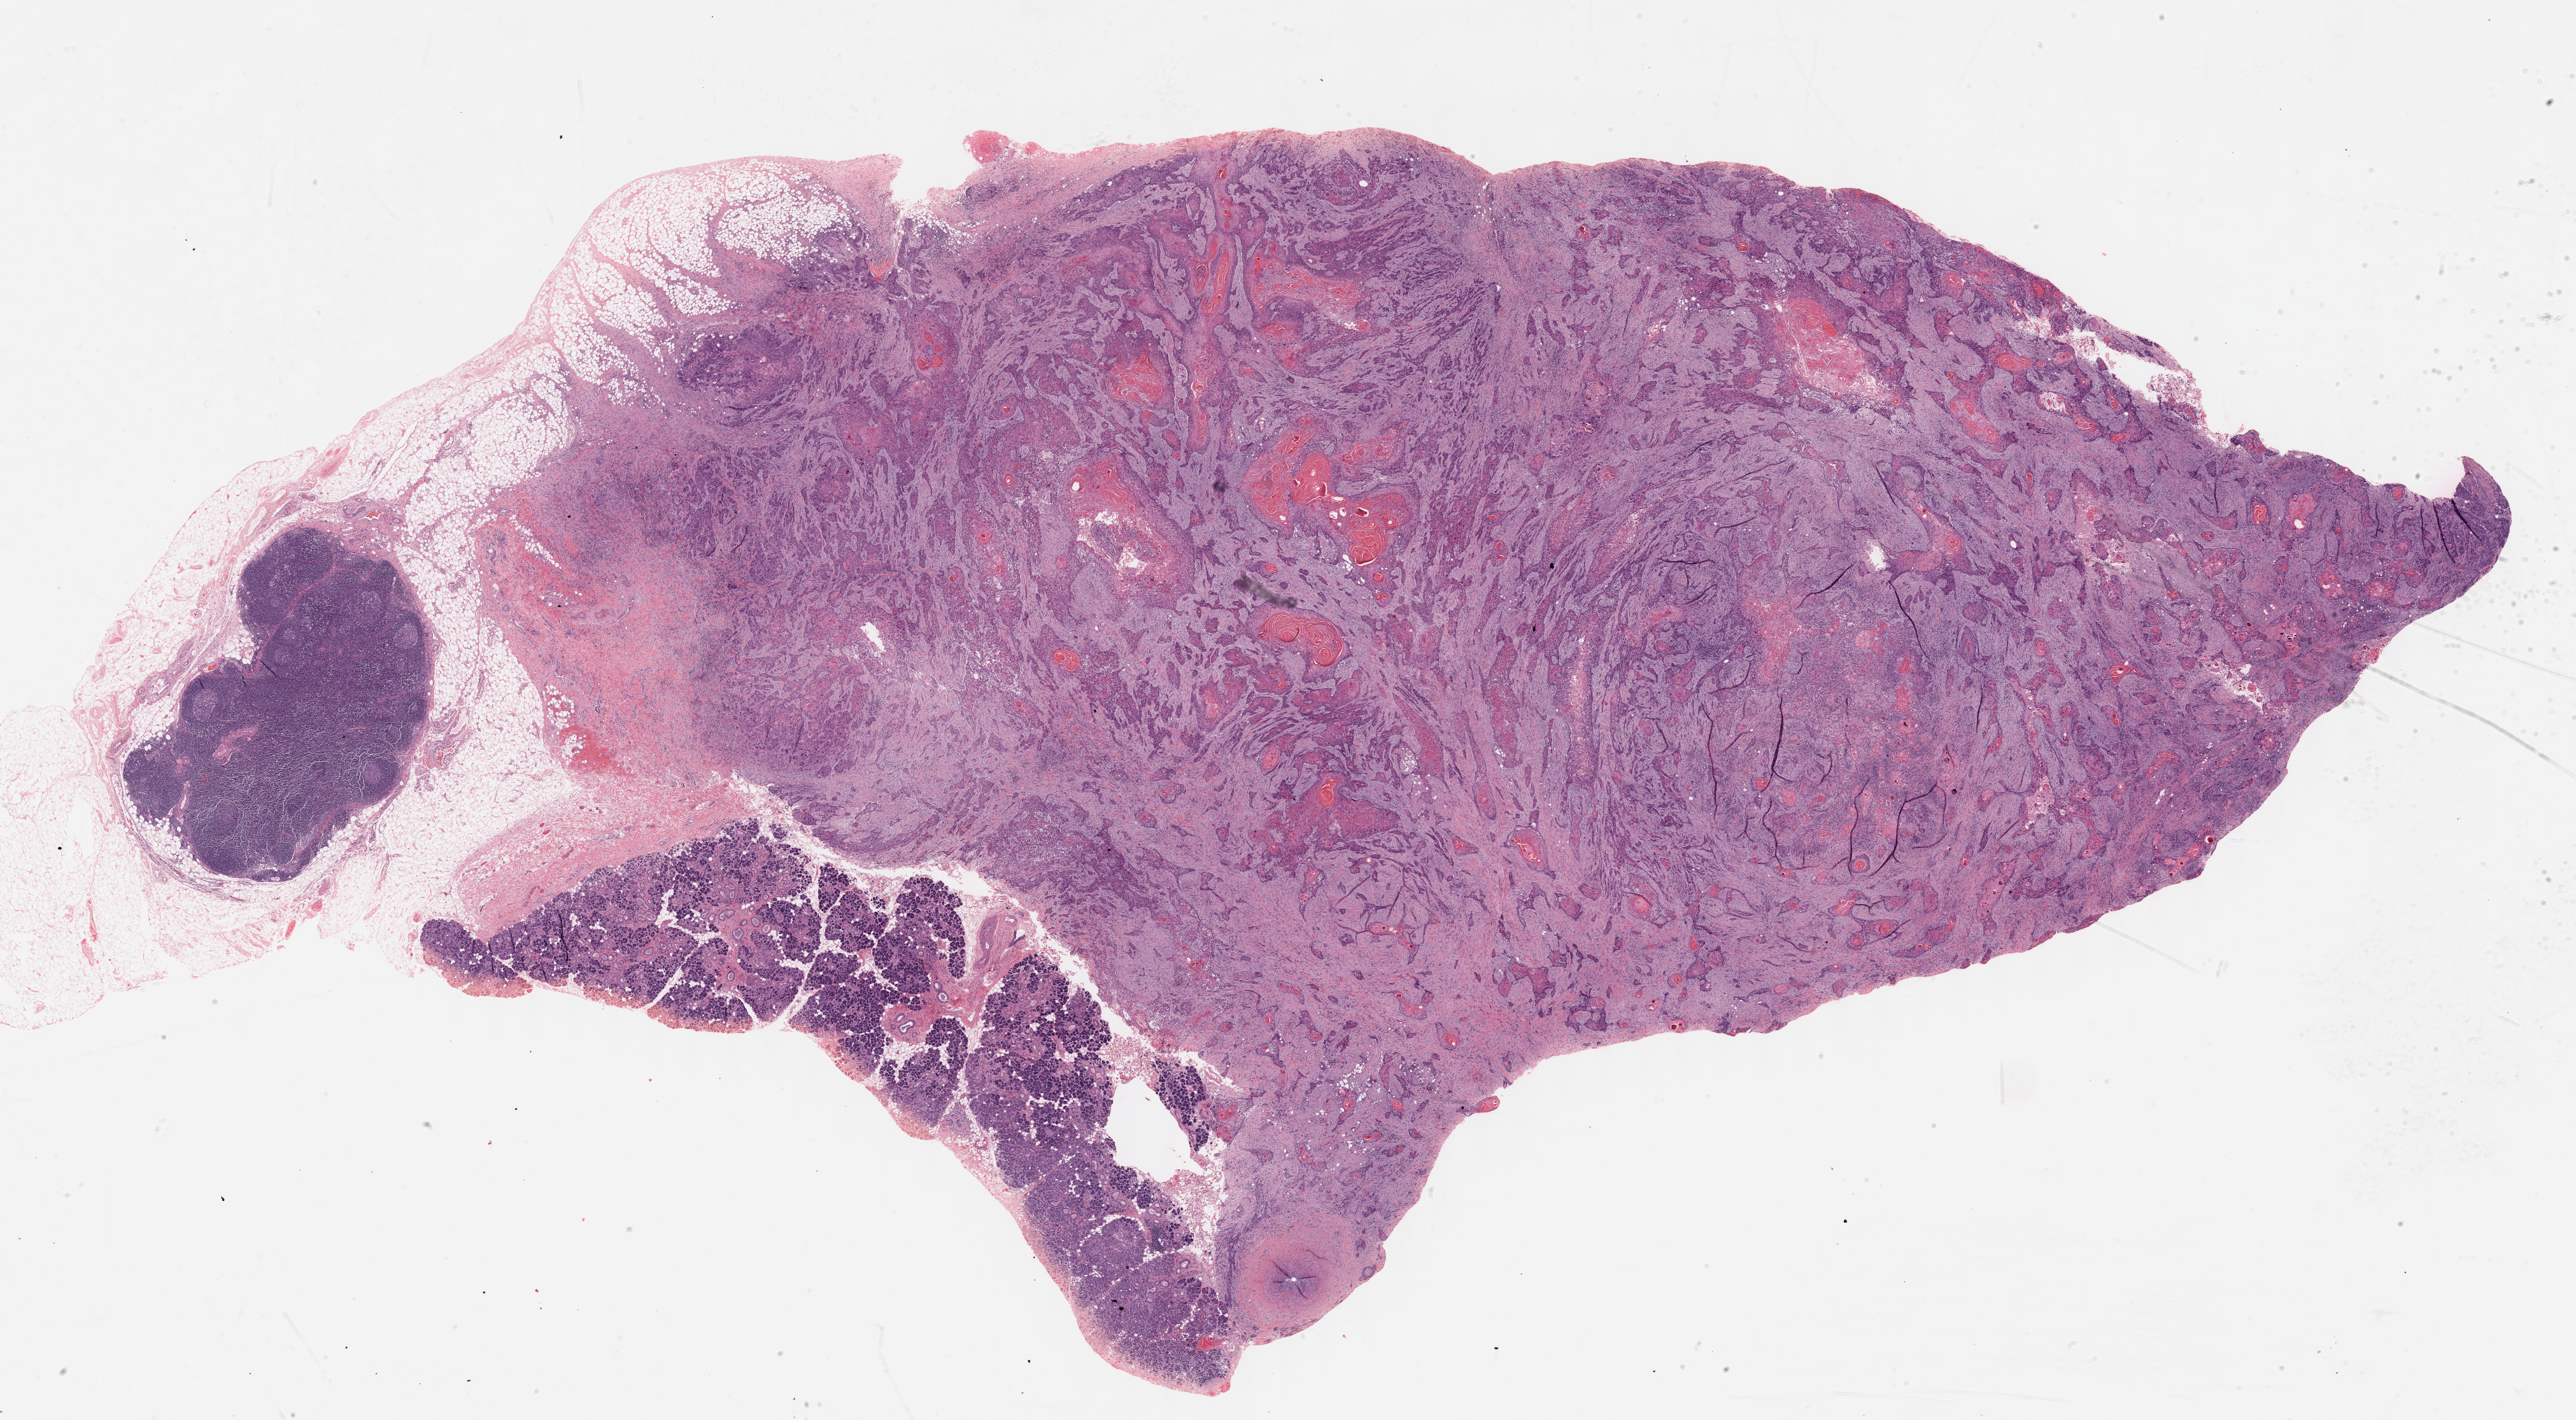
Digitized H&E-stained tissue section (whole slide) — low-resolution overview of the scanned area, about 32.7 x 18.0 mm (from a 40x scan). Formalin-fixed paraffin-embedded (FFPE) diagnostic section. Head and neck, primary tumour sample. Patient: female, age at initial diagnosis 87 years. Histologic grade: G2 (moderately differentiated).
AJCC pathologic stage: II (7th edition). Histologic diagnosis: Squamous cell carcinoma, NOS (overlapping lesion of lip, oral cavity and pharynx).